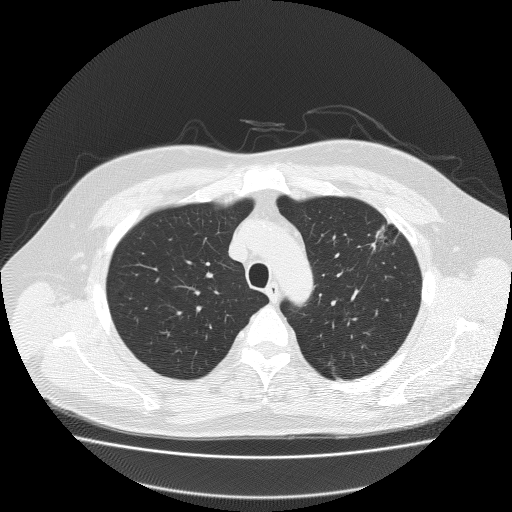
Chest CT (low-dose screening protocol), one axial image. Baseline screening round. Lung window (W 1500 / L -600 HU). Lung (sharp) reconstruction kernel (FC51). 120 kVp. Slice 47 of 204 in the series. 512 × 512 image matrix, field of view 410 × 410 mm. Male participant, aged 62 years at enrolment. Former smoker at enrolment.
Expert-annotated lung lesion, box from (x=348, y=215) to (x=415, y=267) px. Screening reader's record for this exam (one nodule recorded; not confirmed to be the boxed lesion): non-calcified nodule or mass ≥4 mm, left upper lobe, 18 × 8 mm, spiculated (stellate) margins, soft tissue attenuation.